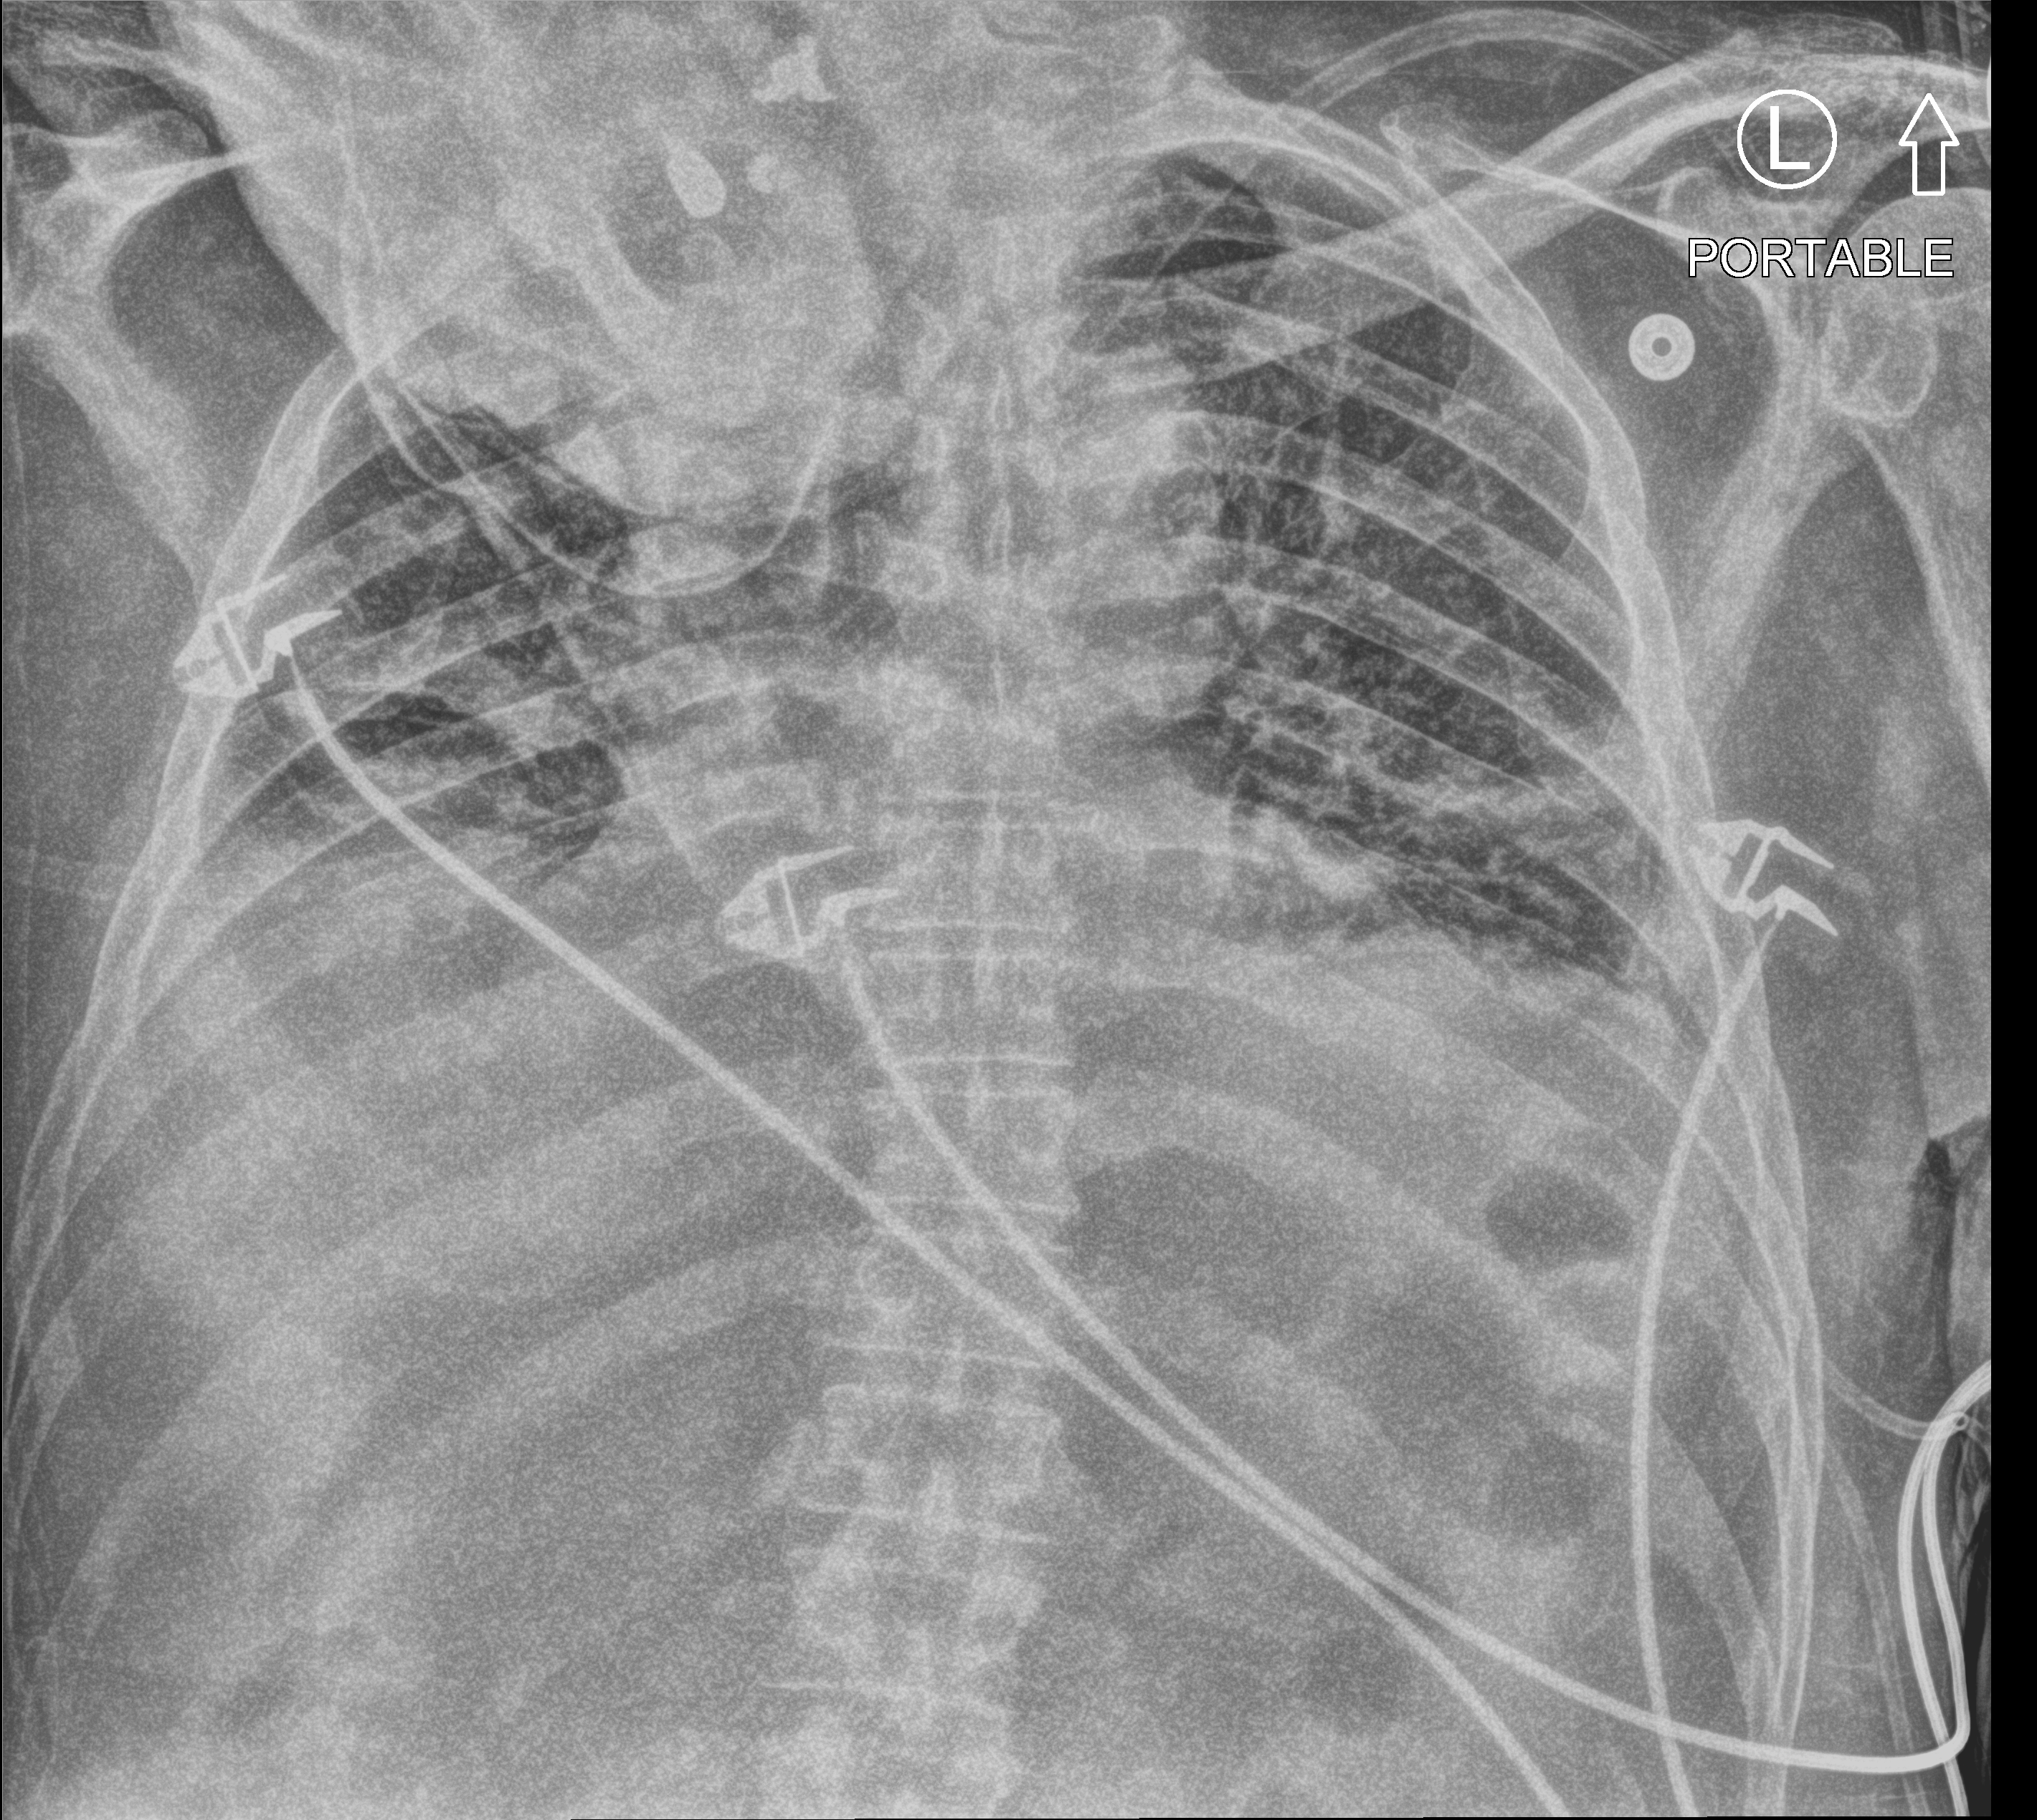
Portable chest radiograph; anteroposterior (AP) projection. Male patient hospitalised with COVID-19, age 60–74 years.
From the hospital-stay record, not from the radiograph (when in the stay this image was taken is not recorded):
- hypertension (admission record): yes